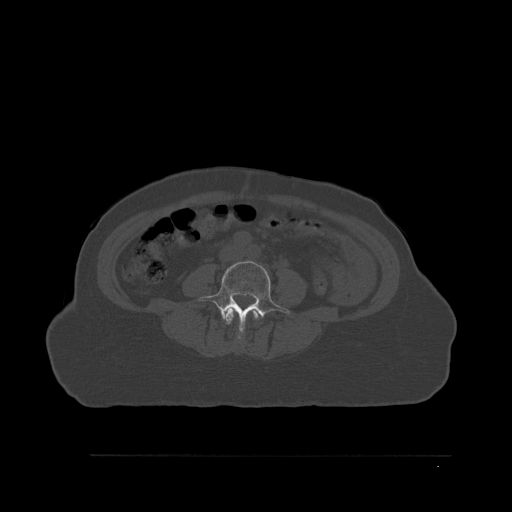
CT including the spine, one axial slice; position 210 of 527 along the scan axis; bone window (W 1800 / L 400 HU); 1.5 mm slice thickness; 512 × 512 image matrix, field of view 470 × 470 mm. Patient: female, 73 years. Case-level facts recorded for this patient, not image findings: primary cancer: breast; vertebrae with lytic lesions (as recorded): L2.
Structures marked on this image (semi-automatically segmented with operator editing):
- L3 vertebra: bounding box <225,307,259,341> (left, top, right, bottom; pixels)
- L4 vertebra: <197,261,290,339>